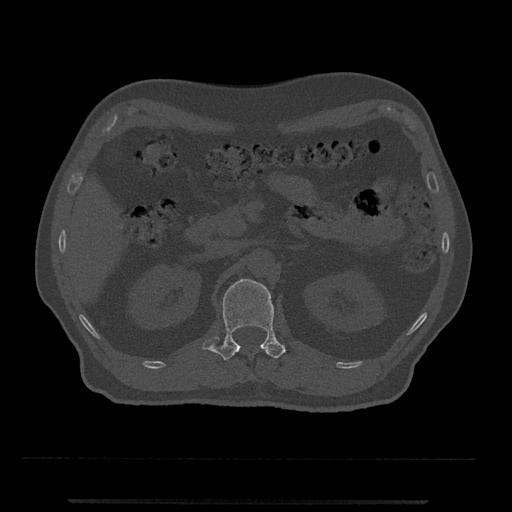
CT including the spine, one axial slice. Slice 347 of 797 in the series (ordered by position). 120 kVp. Bone window (W 1800 / L 400 HU). 0.5 mm slice thickness. 512 × 512 image matrix, field of view 419 × 419 mm. Male patient, age 63 years. Case-level facts recorded for this patient, not image findings: primary cancer: prostate.
Outlined on this slice (semi-automatic segmentation, software-assisted and operator-edited):
- L1 vertebra: bounding box <202,279,286,361> (left, top, right, bottom; pixels)